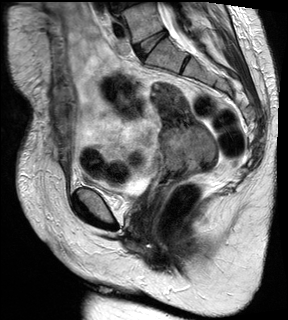
Pelvic MRI for cervical cancer, one sagittal slice; position 13 of 28 along the scan axis; T2-weighted; 1.5 T; TE 89 ms, TR 2740 ms; 4 mm slice thickness; 288 × 320 image matrix. Female patient, age 59 years.
Outlined on this slice (manually delineated by an expert):
- uterus and cervix: bounding box [x1, y1, x2, y2] px = [150, 82, 219, 178]